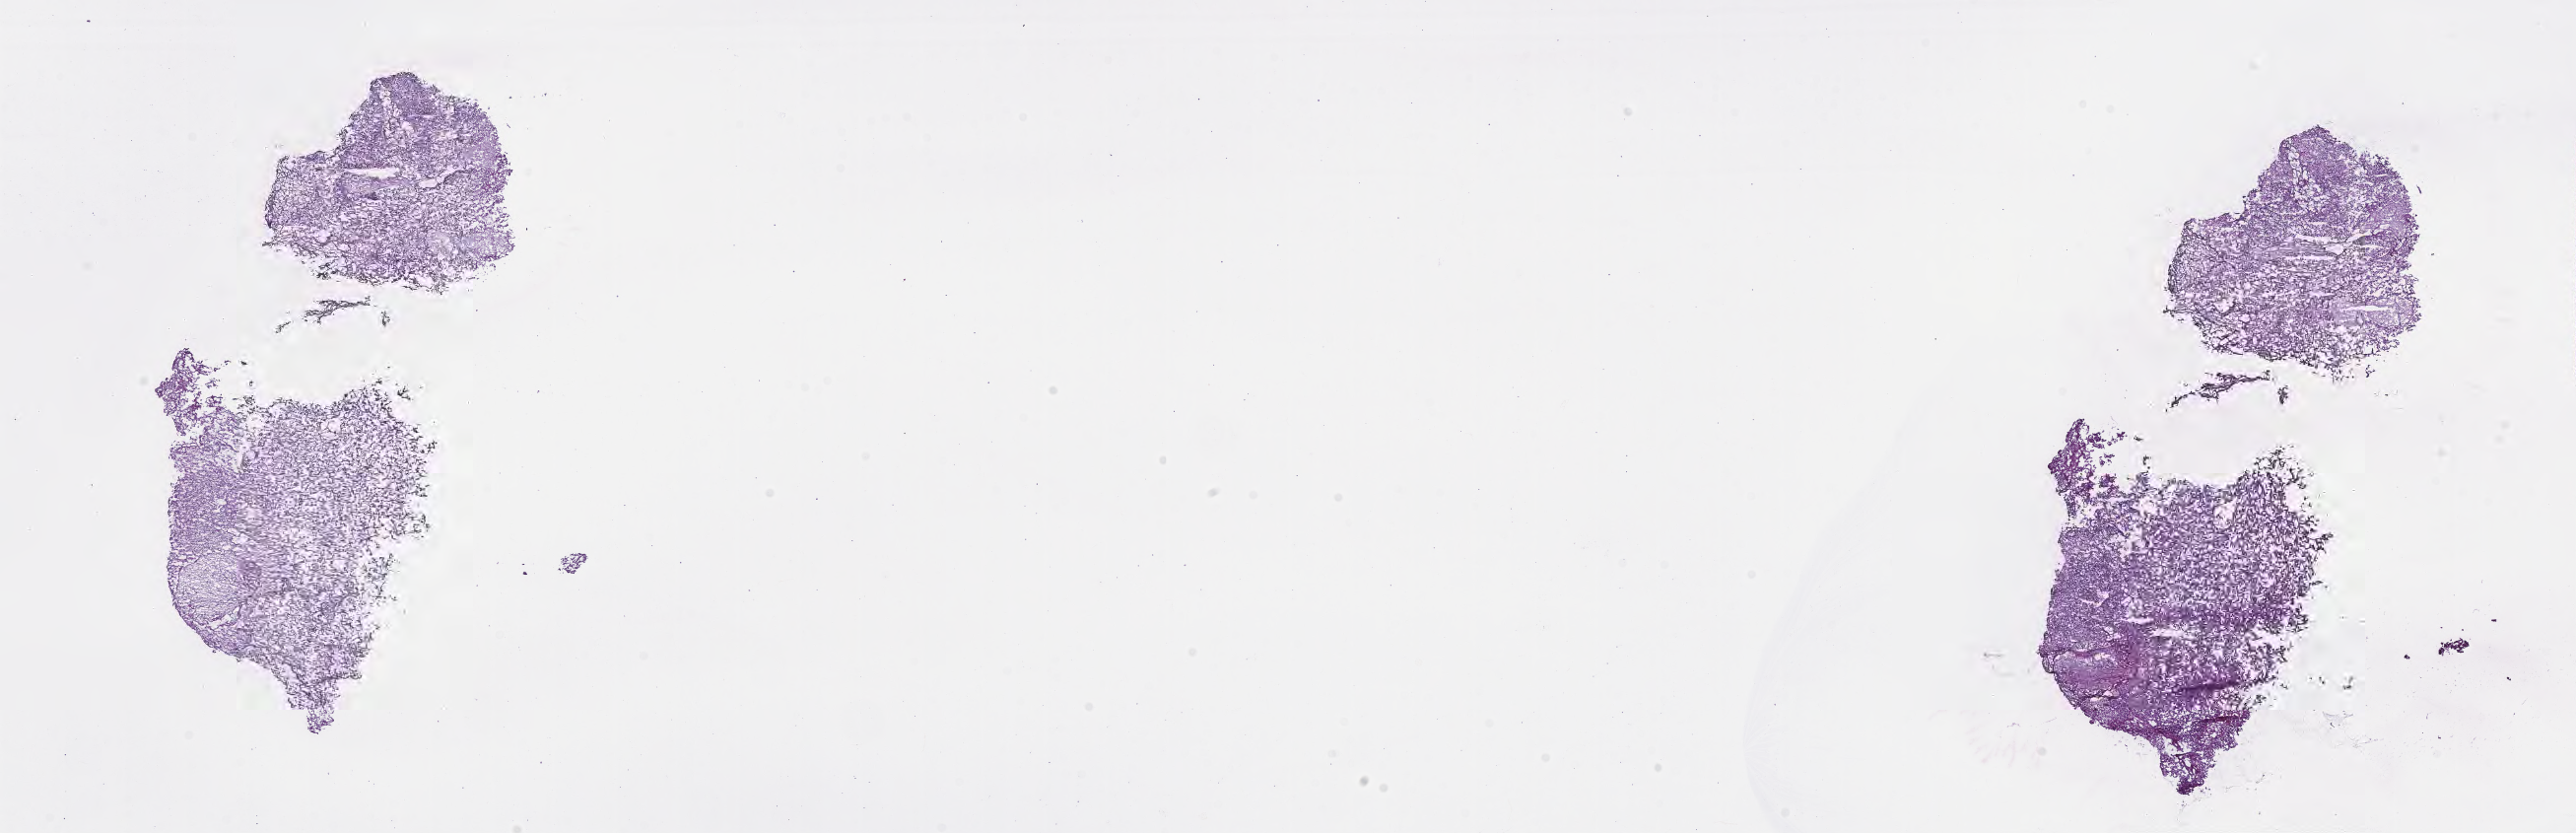
Whole-slide image, H&E stain of tumor tissue from the ovary — whole scanned area (about 21.1 x 6.8 mm) shown as a low-resolution overview. Frozen section. Female patient, age 334 days.
Recorded diagnosis: Granulosa cell tumor, juvenile.